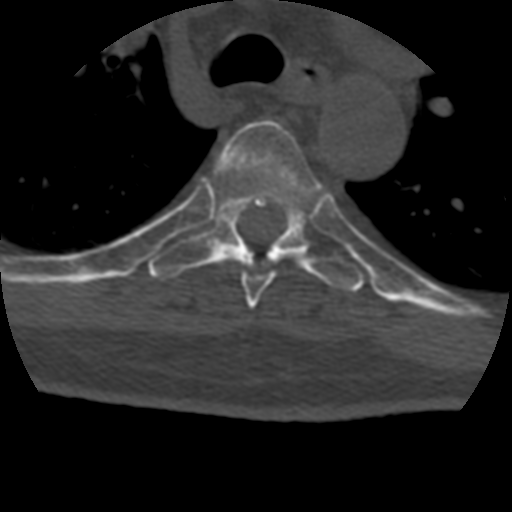
CT including the spine, one axial slice; slice 310 of 399 in the series (ordered by position); 120 kVp; bone window (W 1800 / L 400 HU); 1.25 mm slice thickness; 512 × 512 image matrix, field of view 160 × 160 mm. Patient age 69 years. Case-level facts recorded for this patient, not image findings: primary cancer: prostate.
Annotated regions visible in this slice (semi-automatic segmentation, software-assisted and operator-edited):
- T5 vertebra: box from (x=214, y=120) to (x=323, y=309) px
- T6 vertebra: (x=148, y=187)–(x=365, y=292)